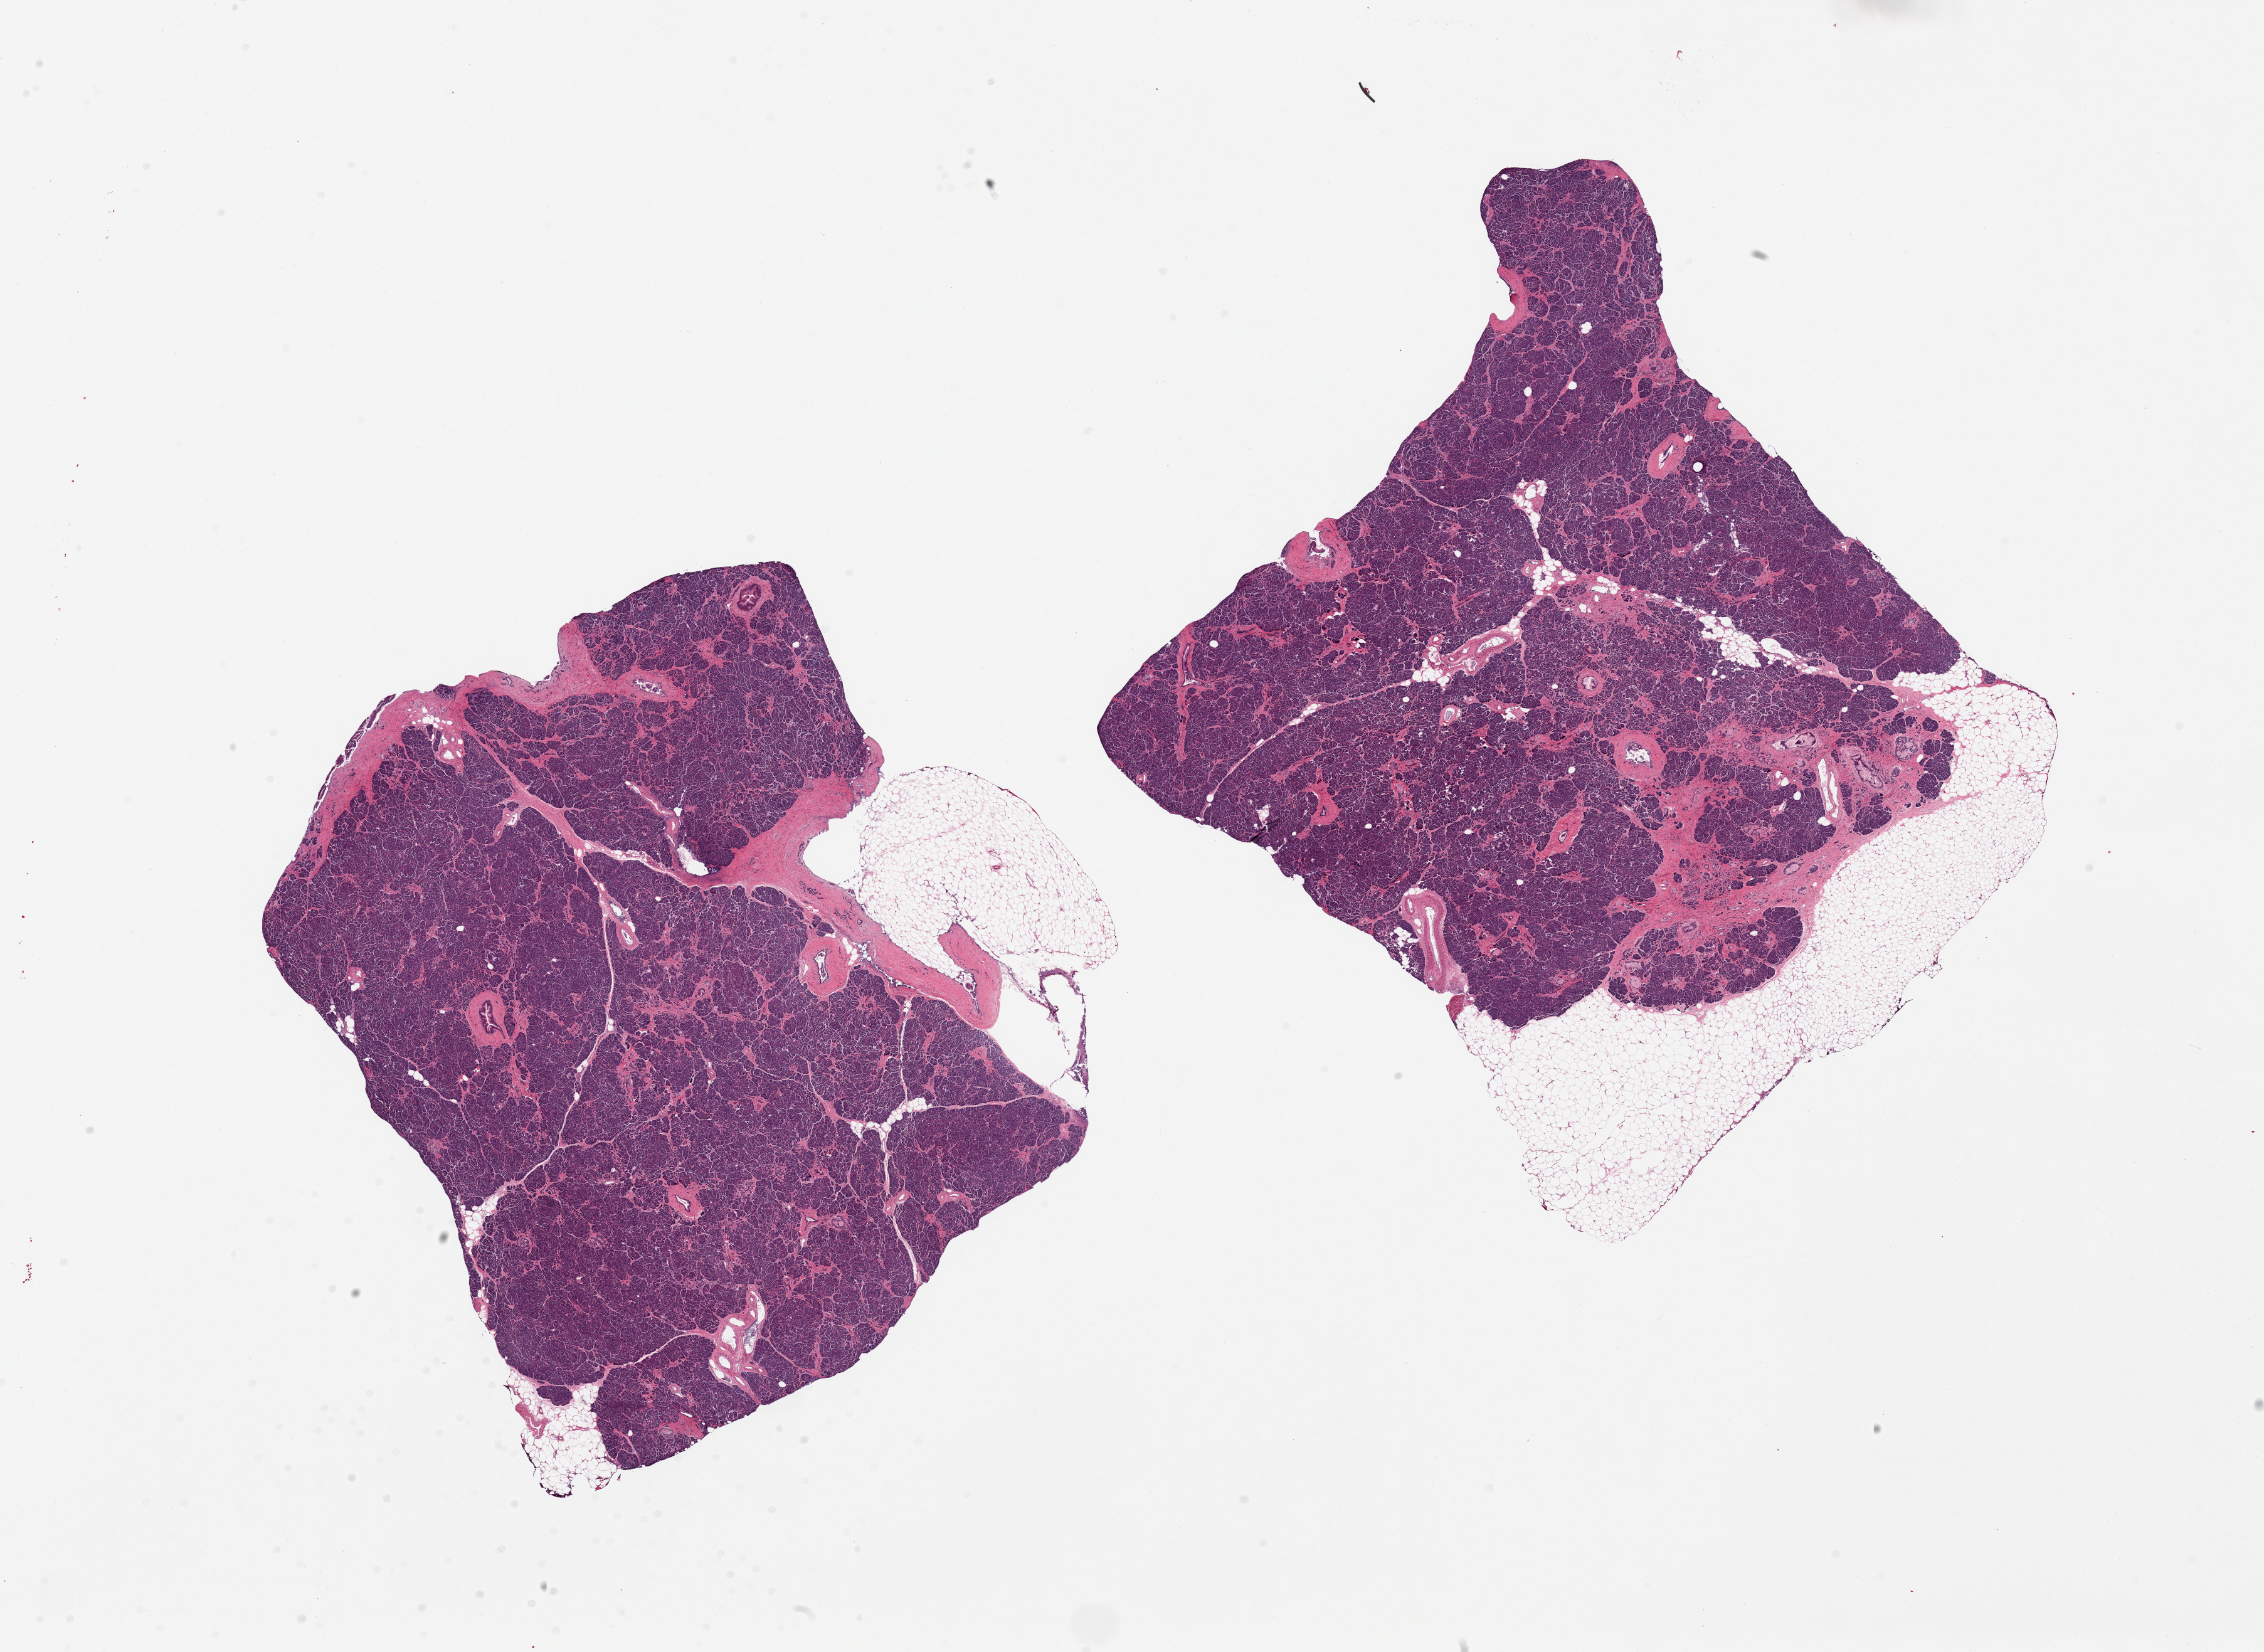
Whole-slide image, hematoxylin and eosin (H&E) stain, shown as a low-resolution overview of the whole scanned area (about 28.5 x 20.8 mm). PAXgene-fixed, paraffin-embedded tissue. Sampled site (target tissue): pancreas. Tissue donor sample.
Reviewer comment on this tissue sample: 2 pieces, 11x9 & 11x10mm; well preserved; Islets rare but visible. Fibrous areas suggest remote pancreatitis.